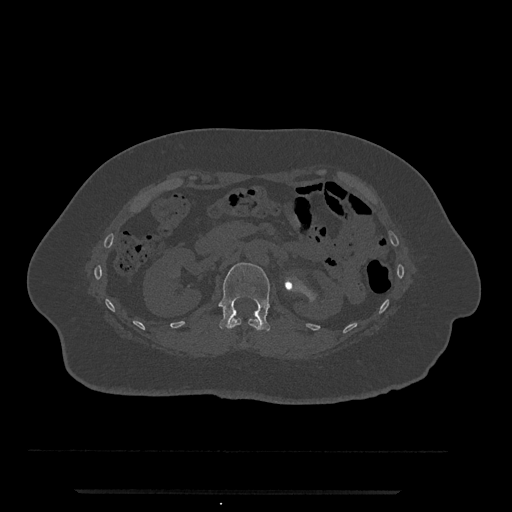
CT including the spine, one axial slice. Slice 121 of 797 in the series (ordered by position). Bone window (W 1800 / L 400 HU). 0.5 mm slice thickness. 512 × 512 image matrix, field of view 440 × 440 mm. Female patient, age 51 years. From the clinical record (not read from this slice): primary cancer: neuro; vertebrae with lytic lesions (as recorded): T8.
Outlined on this slice (semi-automatic segmentation, software-assisted and operator-edited):
- L1 vertebra: bounding box <219,263,270,331> (left, top, right, bottom; pixels)
- T12 vertebra: <227,318,262,331>